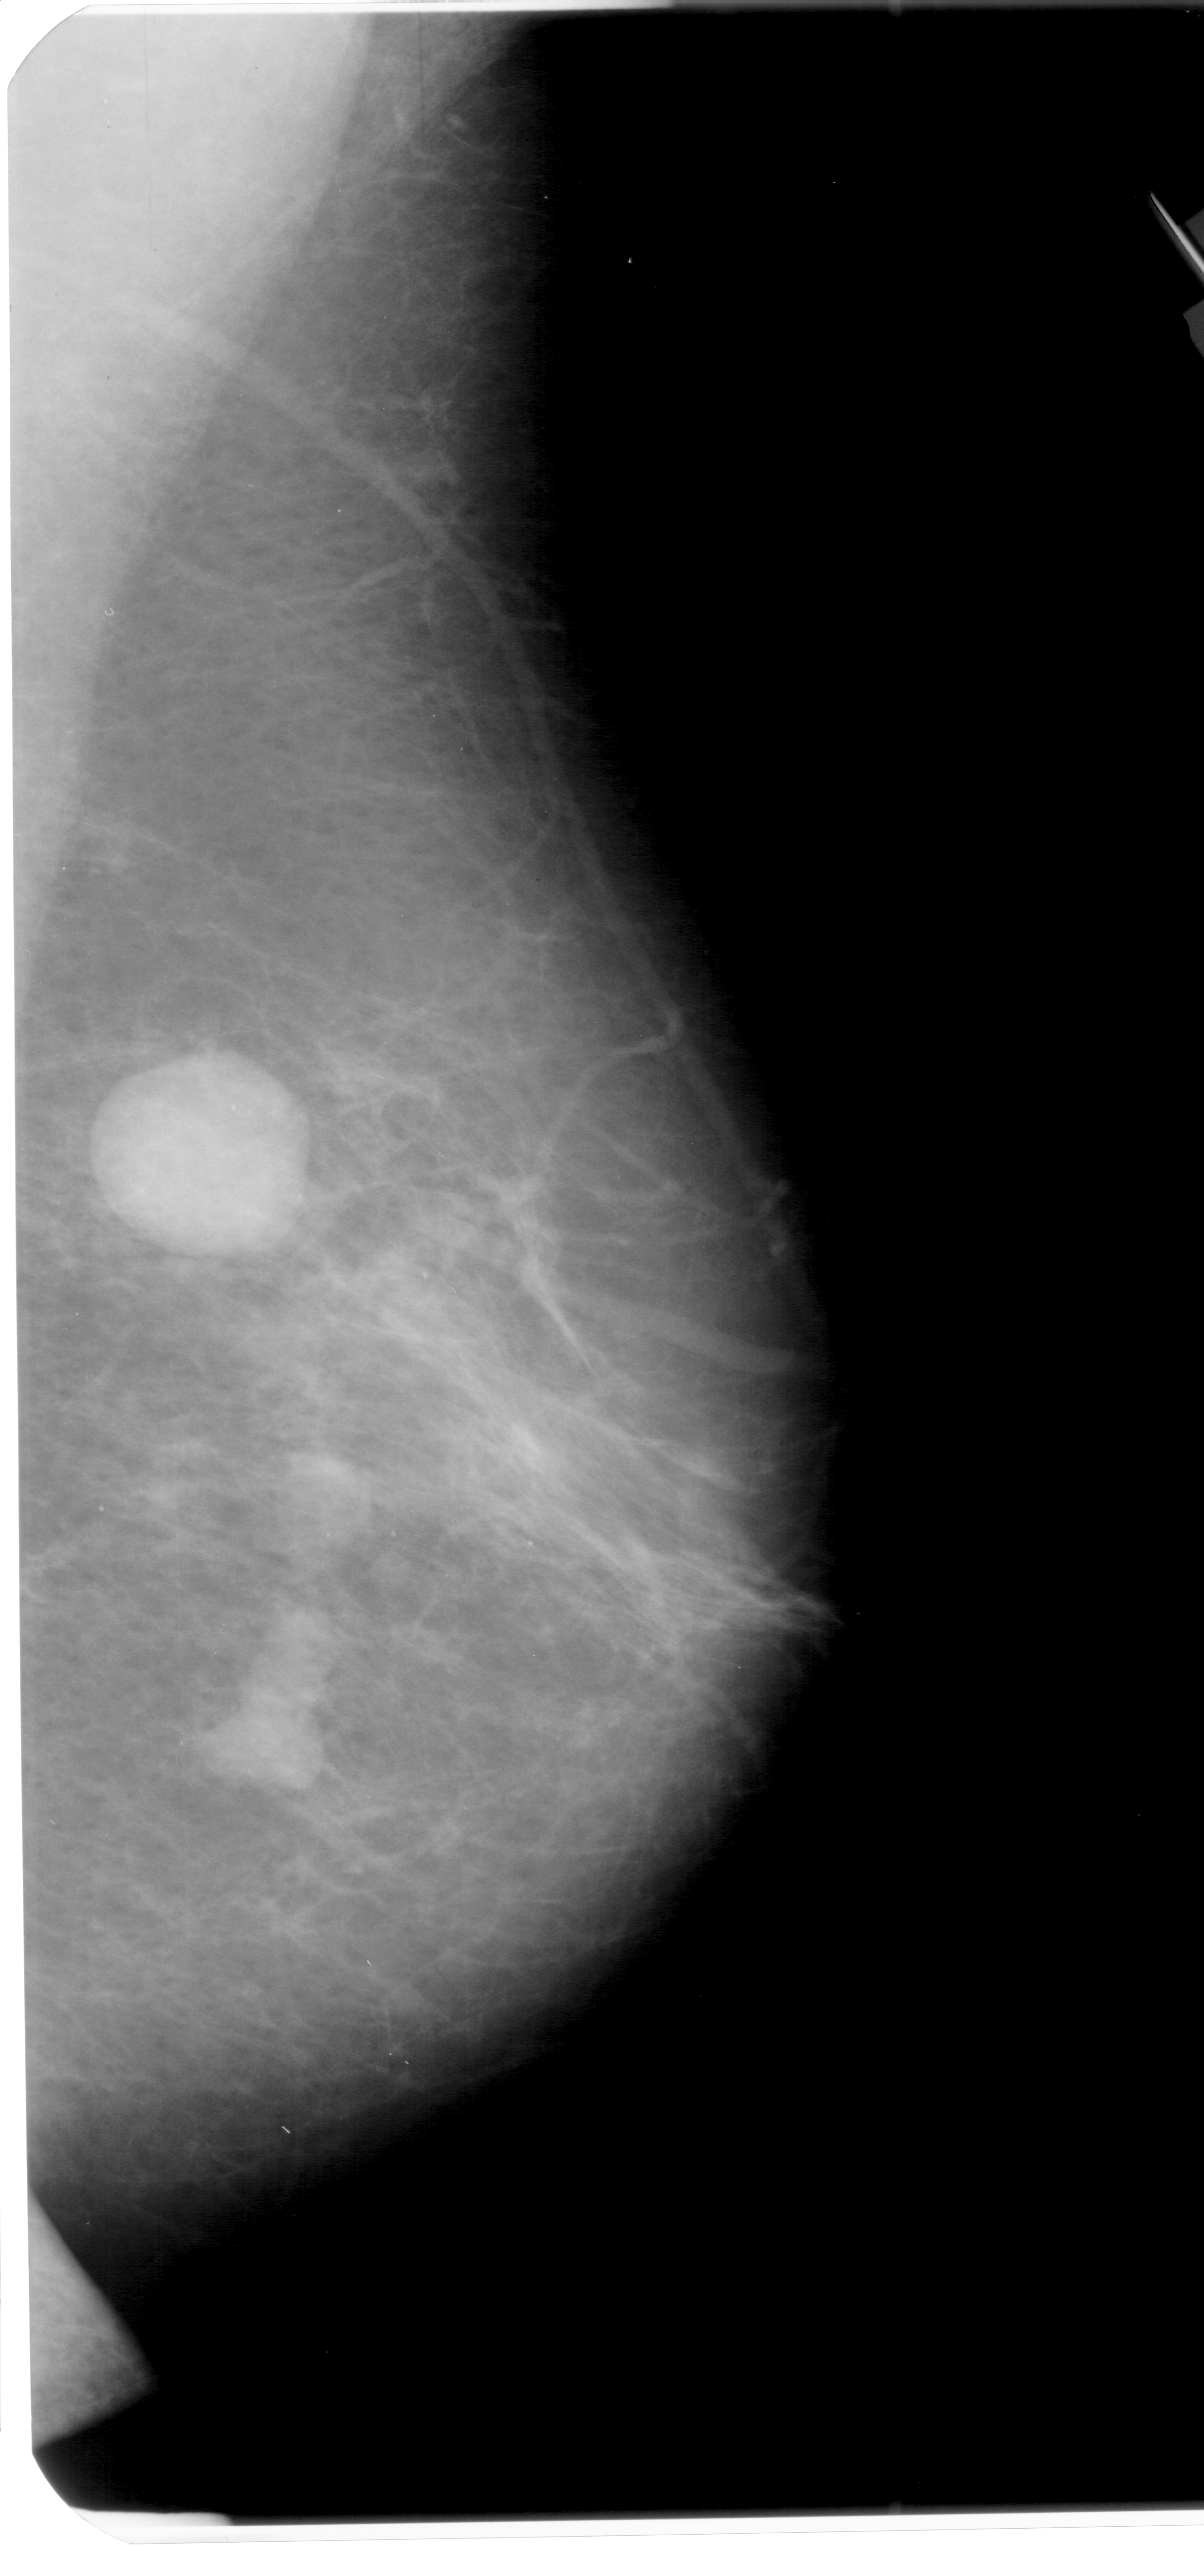
Digitized screen-film mammogram, right breast, MLO view, BI-RADS breast density category 2 (scale 1–4).
Marked findings (only marked abnormalities are described; nothing is implied about the rest of the image): Finding 1 of 2: mass, shape oval, margins ill defined; BI-RADS assessment category 4; pathology result (as recorded, not read from the image): malignant. Finding 2 of 2: mass, shape oval, margins ill defined; BI-RADS assessment category 4; subtlety rating 5 on a 1 (subtle) to 5 (obvious) scale; pathology result (as recorded, not read from the image): malignant.